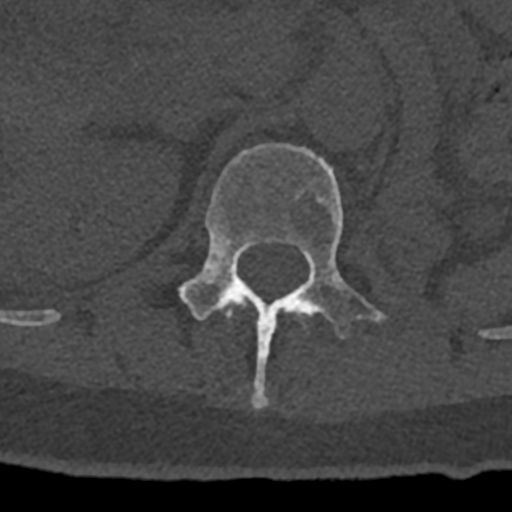
CT including the spine, one axial slice. Position 444 of 797 along the scan axis. Reconstruction kernel Br40s/3. Bone window (W 1800 / L 400 HU). 512 × 512 image matrix. Male patient, age 74 years. From the clinical record (not read from this slice): primary cancer: renal.
Structures marked on this image (semi-automatic segmentation, software-assisted and operator-edited):
- L1 vertebra: box from (x=178, y=144) to (x=386, y=410) px
- T12 vertebra: (x=222, y=299)–(x=247, y=318)